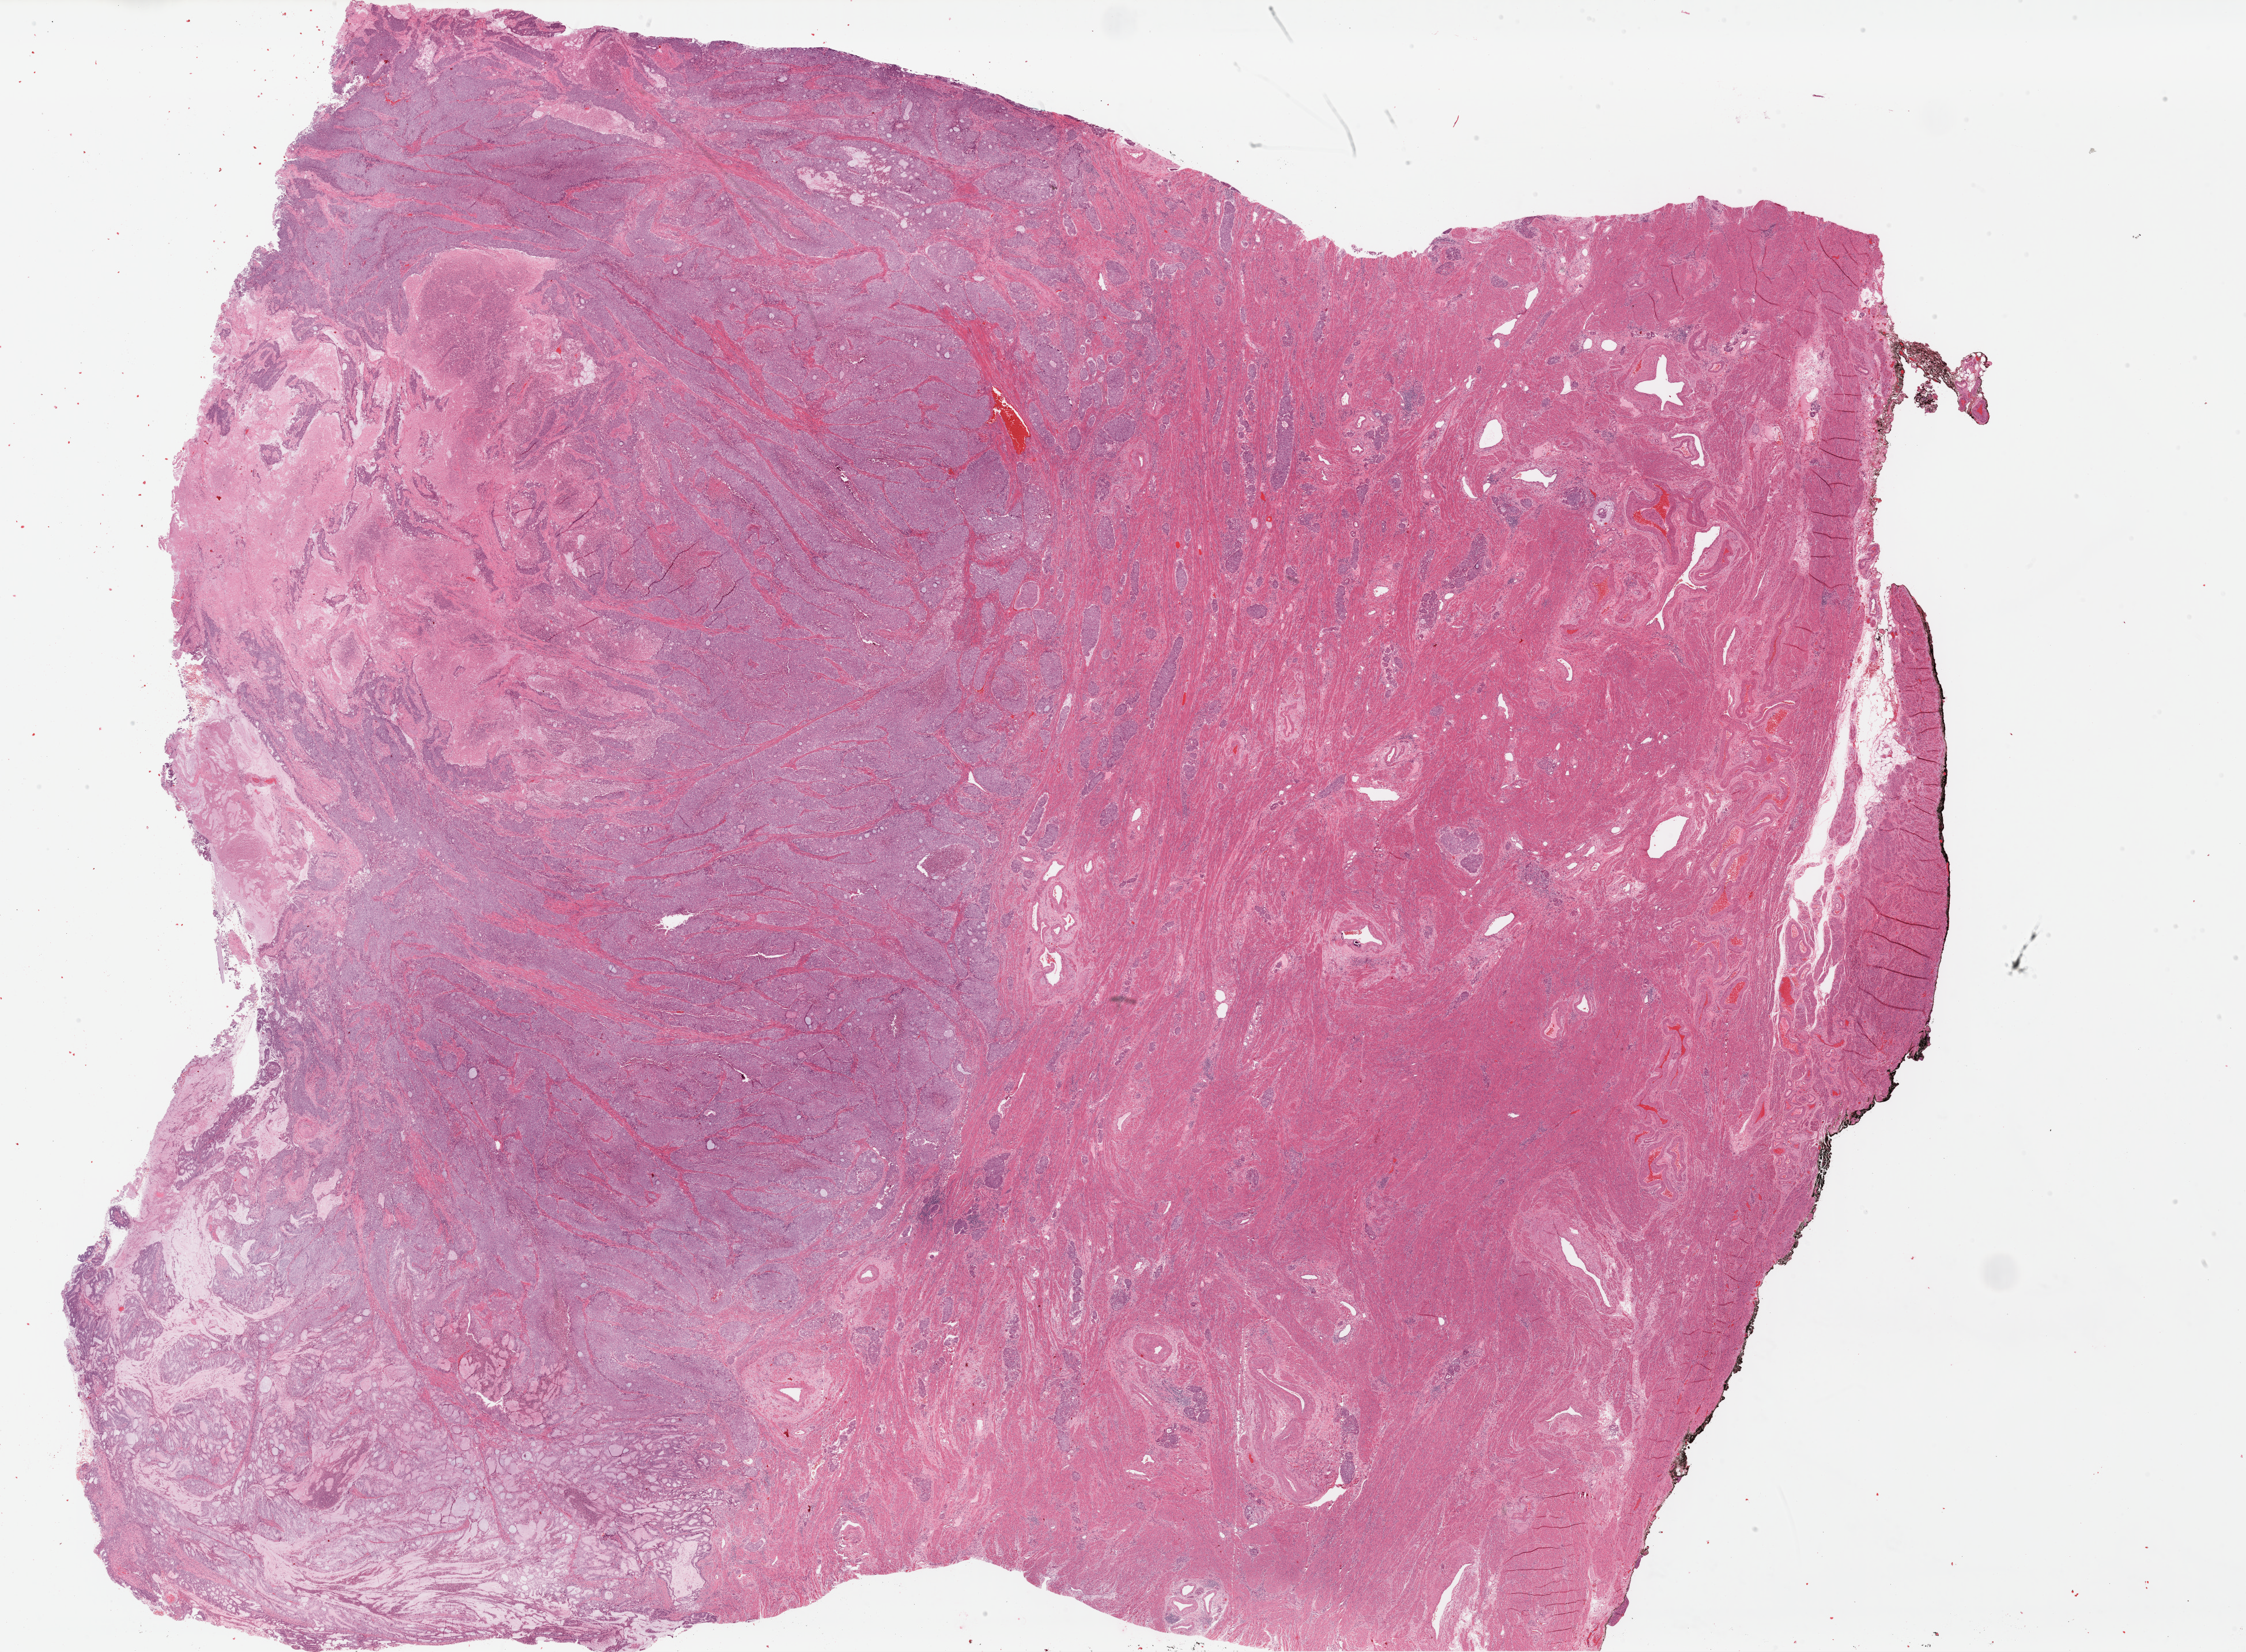
Whole-slide histology image, H&E — low-resolution overview of the scanned area, about 30.8 x 22.6 mm, formalin-fixed paraffin-embedded (FFPE) diagnostic section, primary tumour sample from the uterus. Female patient; age at initial diagnosis 77 years.
Diagnosis: Endometrioid adenocarcinoma, NOS (endometrium).